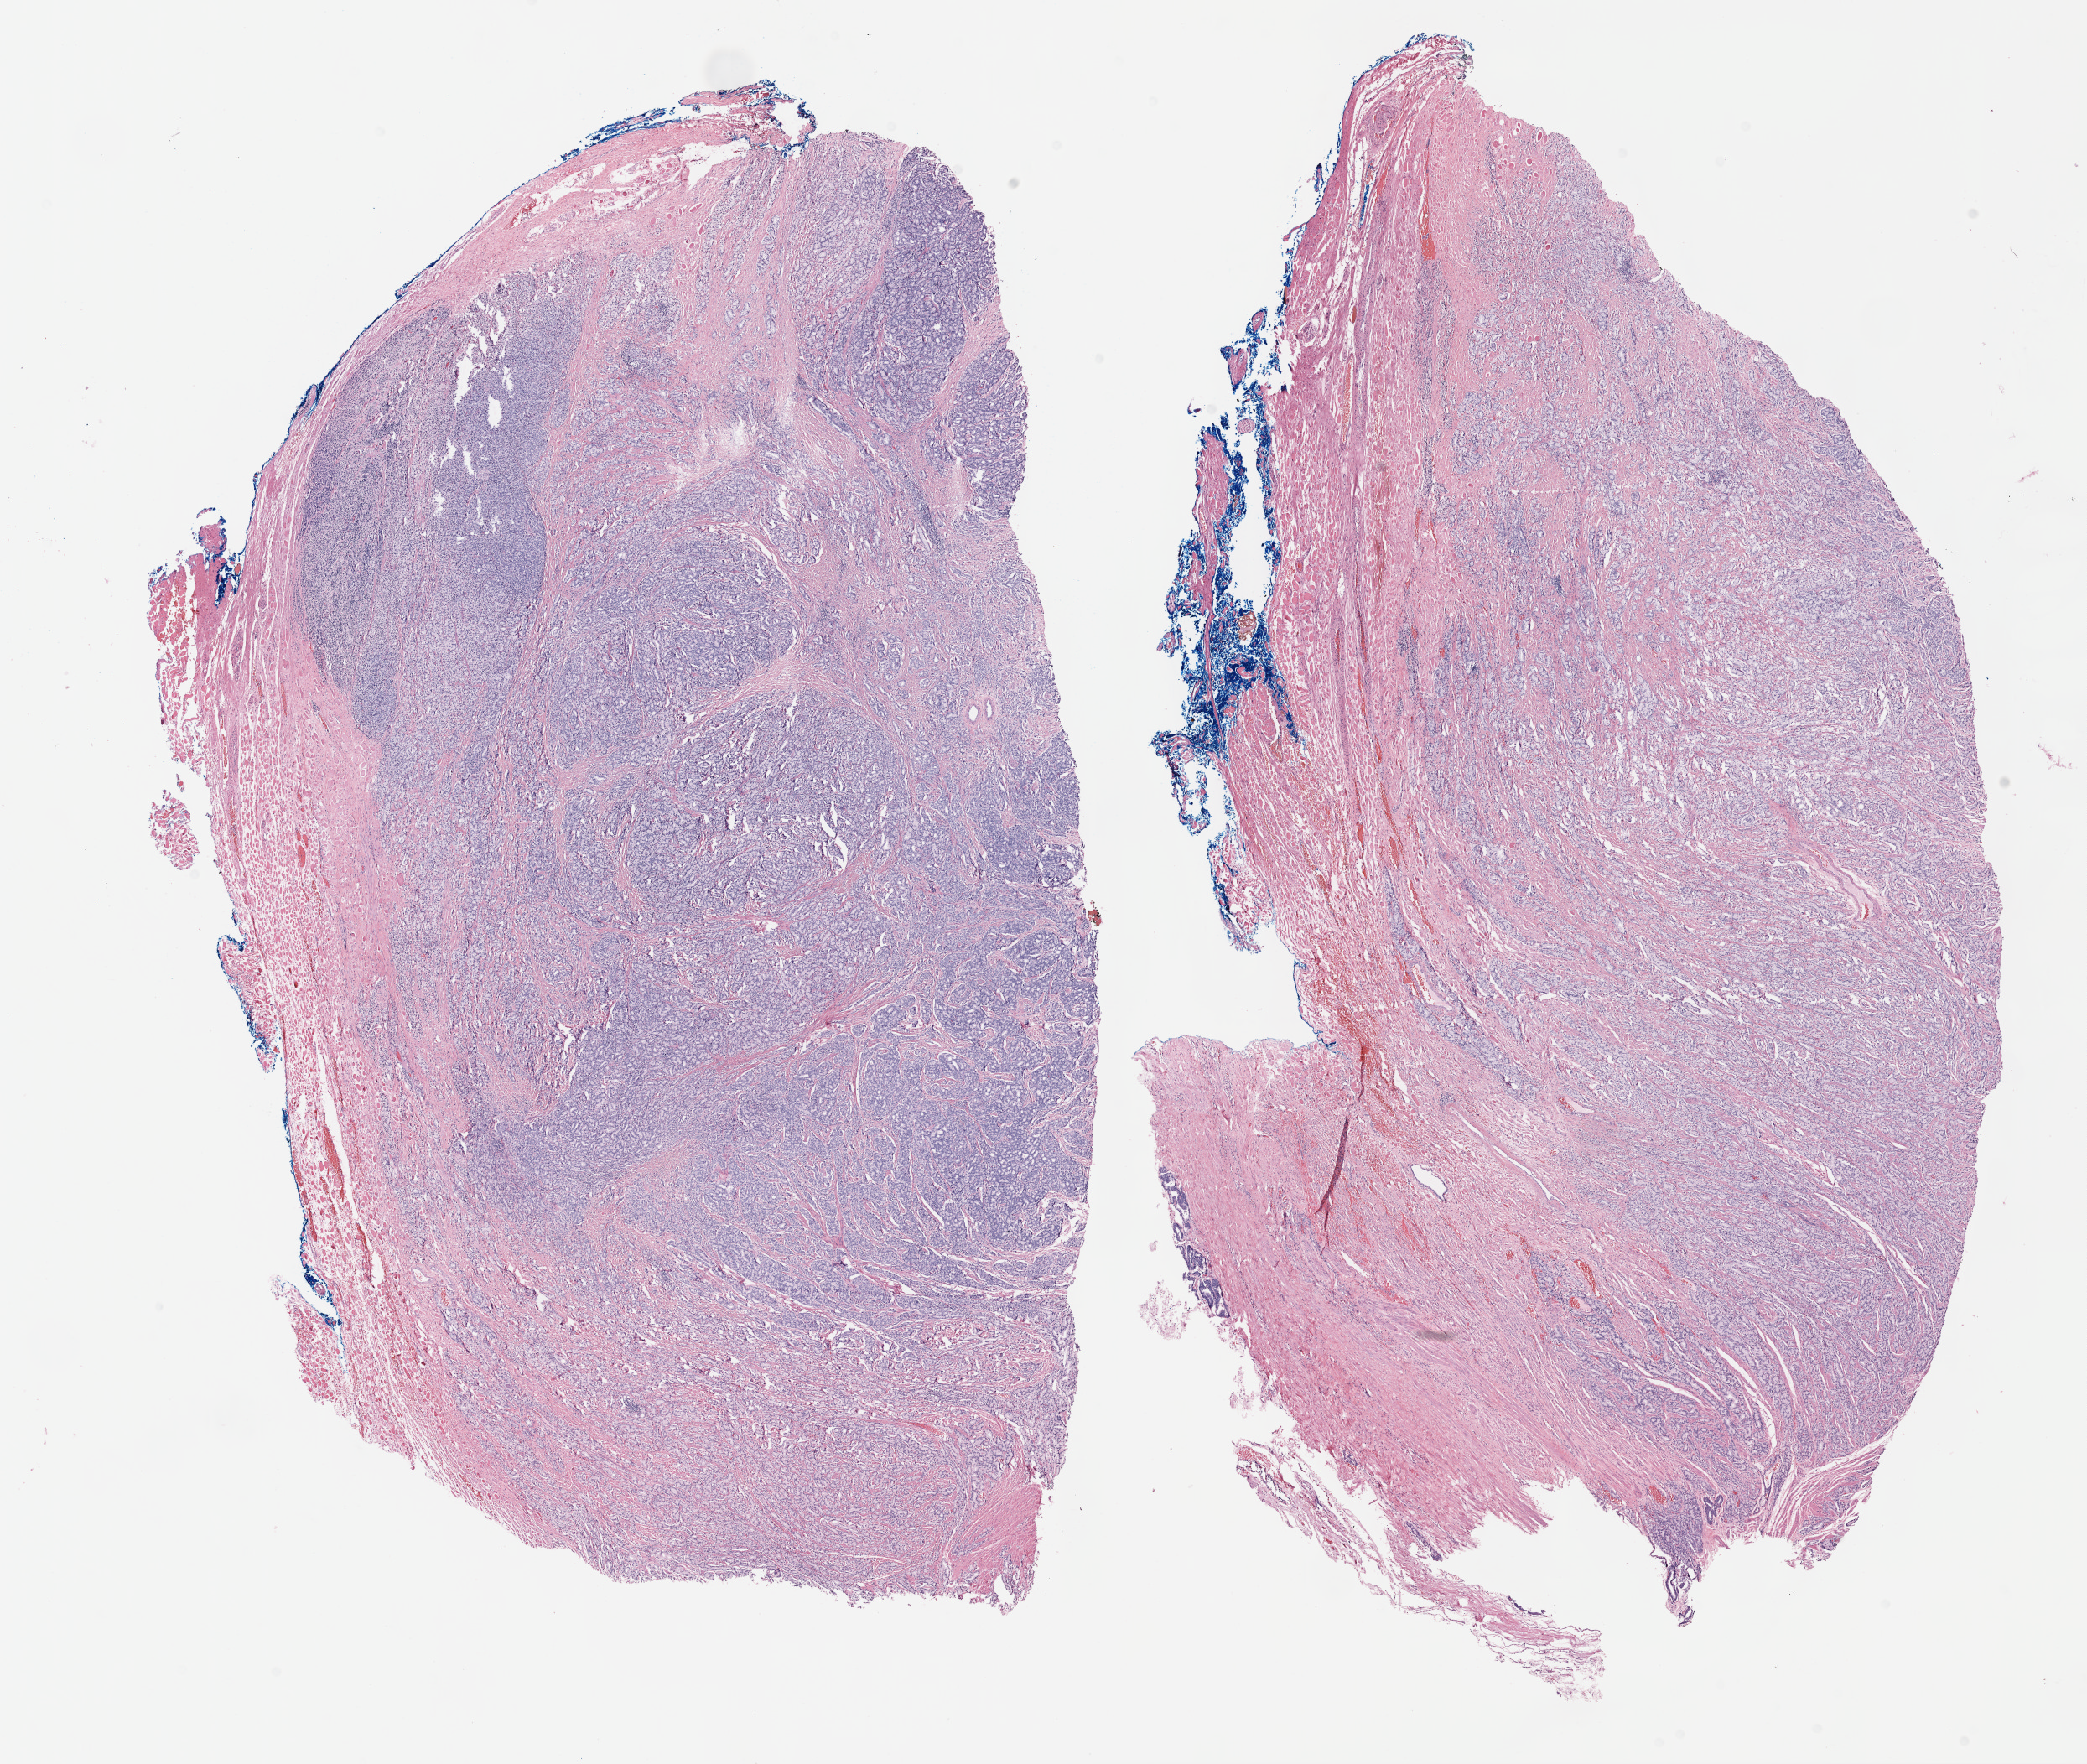
Digitized H&E-stained tissue section (whole slide), a low-resolution overview of the entire scanned area, about 20.1 x 17.0 mm (from a 40x scan). Formalin-fixed paraffin-embedded (FFPE) diagnostic section. Prostate, primary tumour sample. Male patient; age at initial diagnosis 70 years. Gleason score: 8 (4+4).
• diagnosis: Adenocarcinoma, NOS (prostate gland)
• lymph nodes positive (case pathology): 0 of 4 examined